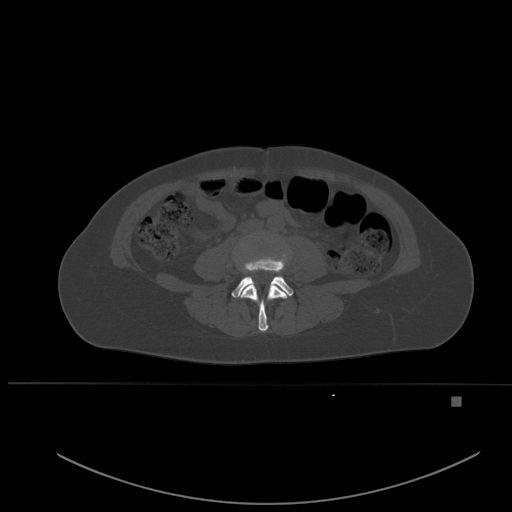
CT including the spine, one axial slice. Position 182 of 651 along the scan axis. Bone window (W 1800 / L 400 HU). 1.5 mm slice thickness. 512 × 512 image matrix, field of view 443 × 443 mm. Female patient, age 49 years. Case-level facts recorded for this patient, not image findings: primary cancer: breast; vertebrae with lytic lesions (as recorded): L3, T12, L4.
Outlined on this slice (semi-automatically segmented with operator editing):
- L3 vertebra: bounding box [x1, y1, x2, y2] px = [239, 270, 288, 332]
- L4 vertebra: [232, 257, 294, 298]